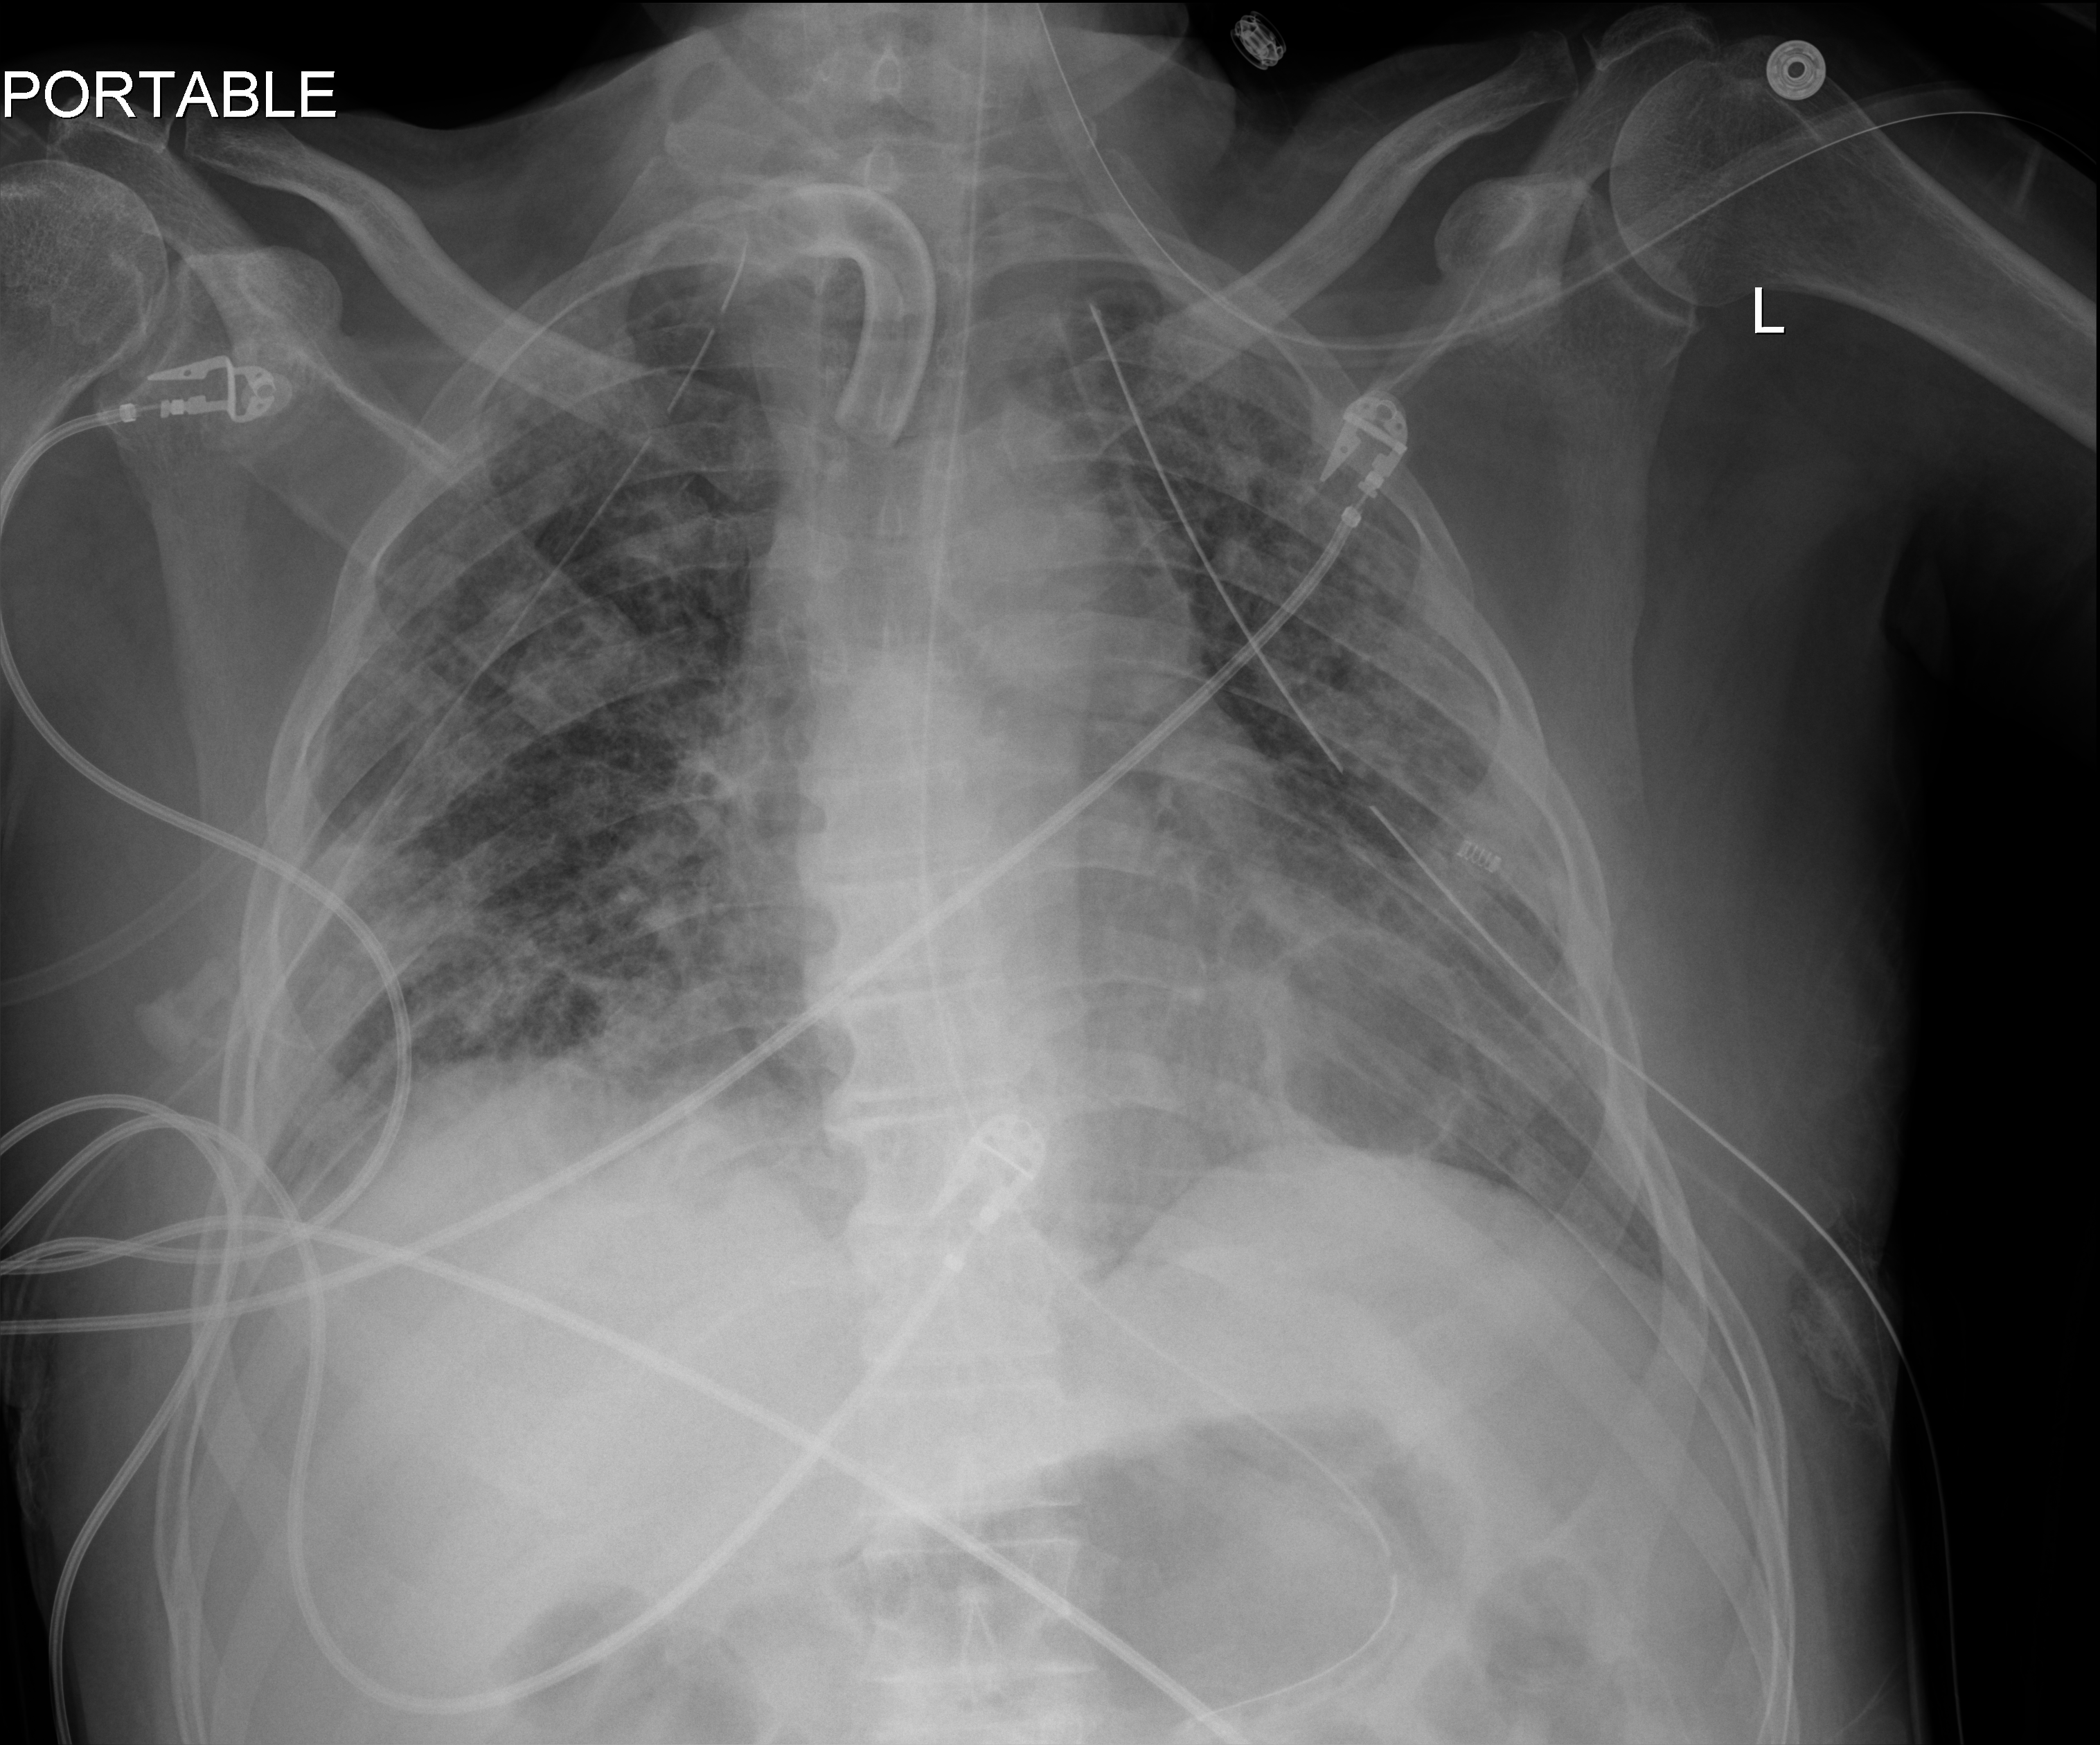
Chest X-ray (portable). Male patient hospitalised with COVID-19, age 18–59 years.
Hospital-stay facts (about this admission, not read from this image; timing relative to this image not recorded): diabetes (admission record): no; length of hospital stay: 83 days.